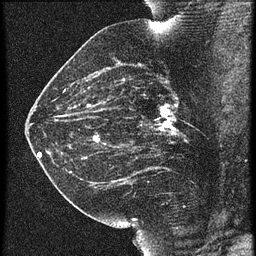
Breast MRI (dynamic contrast-enhanced), one sagittal slice; slice 32 of 60 in the series (ordered by position); 3 images stored at this slice position (order not interpretable as contrast timing); 1.5 T; TE 4.2 ms, TR 21.3 ms; 256 × 256 image matrix. Patient: female, 42 years. Case-level facts recorded for this patient, not image findings: setting: breast cancer imaged before/during neoadjuvant chemotherapy; receptor status: HER2-positive.
Structures marked on this image (semi-automatic segmentation, software-assisted and operator-edited):
- analysis volume of interest (the breast-tissue region the enhancement analysis was run in; not a lesion): bounding box <122,82,195,147> (left, top, right, bottom; pixels)
- tumour enhancement mask (voxels above the 90 % enhancement threshold inside the analysis volume of interest): <157,104,176,131>